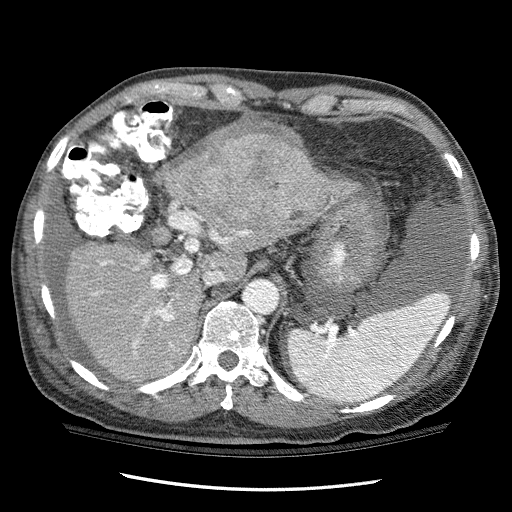
Contrast-enhanced abdominal CT (liver protocol), one axial slice. Position 76 of 114 along the scan axis. Reconstruction kernel STANDARD. 120 kVp. One of 3 acquisitions stored at this slice position. Soft-tissue window (W 400 / L 40 HU). 2.5 mm slice thickness. 512 × 512 image matrix, field of view 360 × 360 mm. From the clinical record (not read from this slice): diagnosis: hepatocellular carcinoma (patient treated with transarterial chemoembolisation; whether this scan precedes or follows treatment is not stated here); TNM stage (as recorded): Stage-I; Child-Pugh class: C; tumour differentiation: well differentiated; tumour nodularity: uninodular.
Structures marked on this image (semi-automatically segmented with operator editing):
- liver parenchyma outside the tumour (the mass and vessels are separate outlines, so this box may not span the whole liver): box from (x=66, y=134) to (x=360, y=382) px
- mass: (x=170, y=135)–(x=354, y=239)
- liver vessels: (x=93, y=230)–(x=249, y=353)